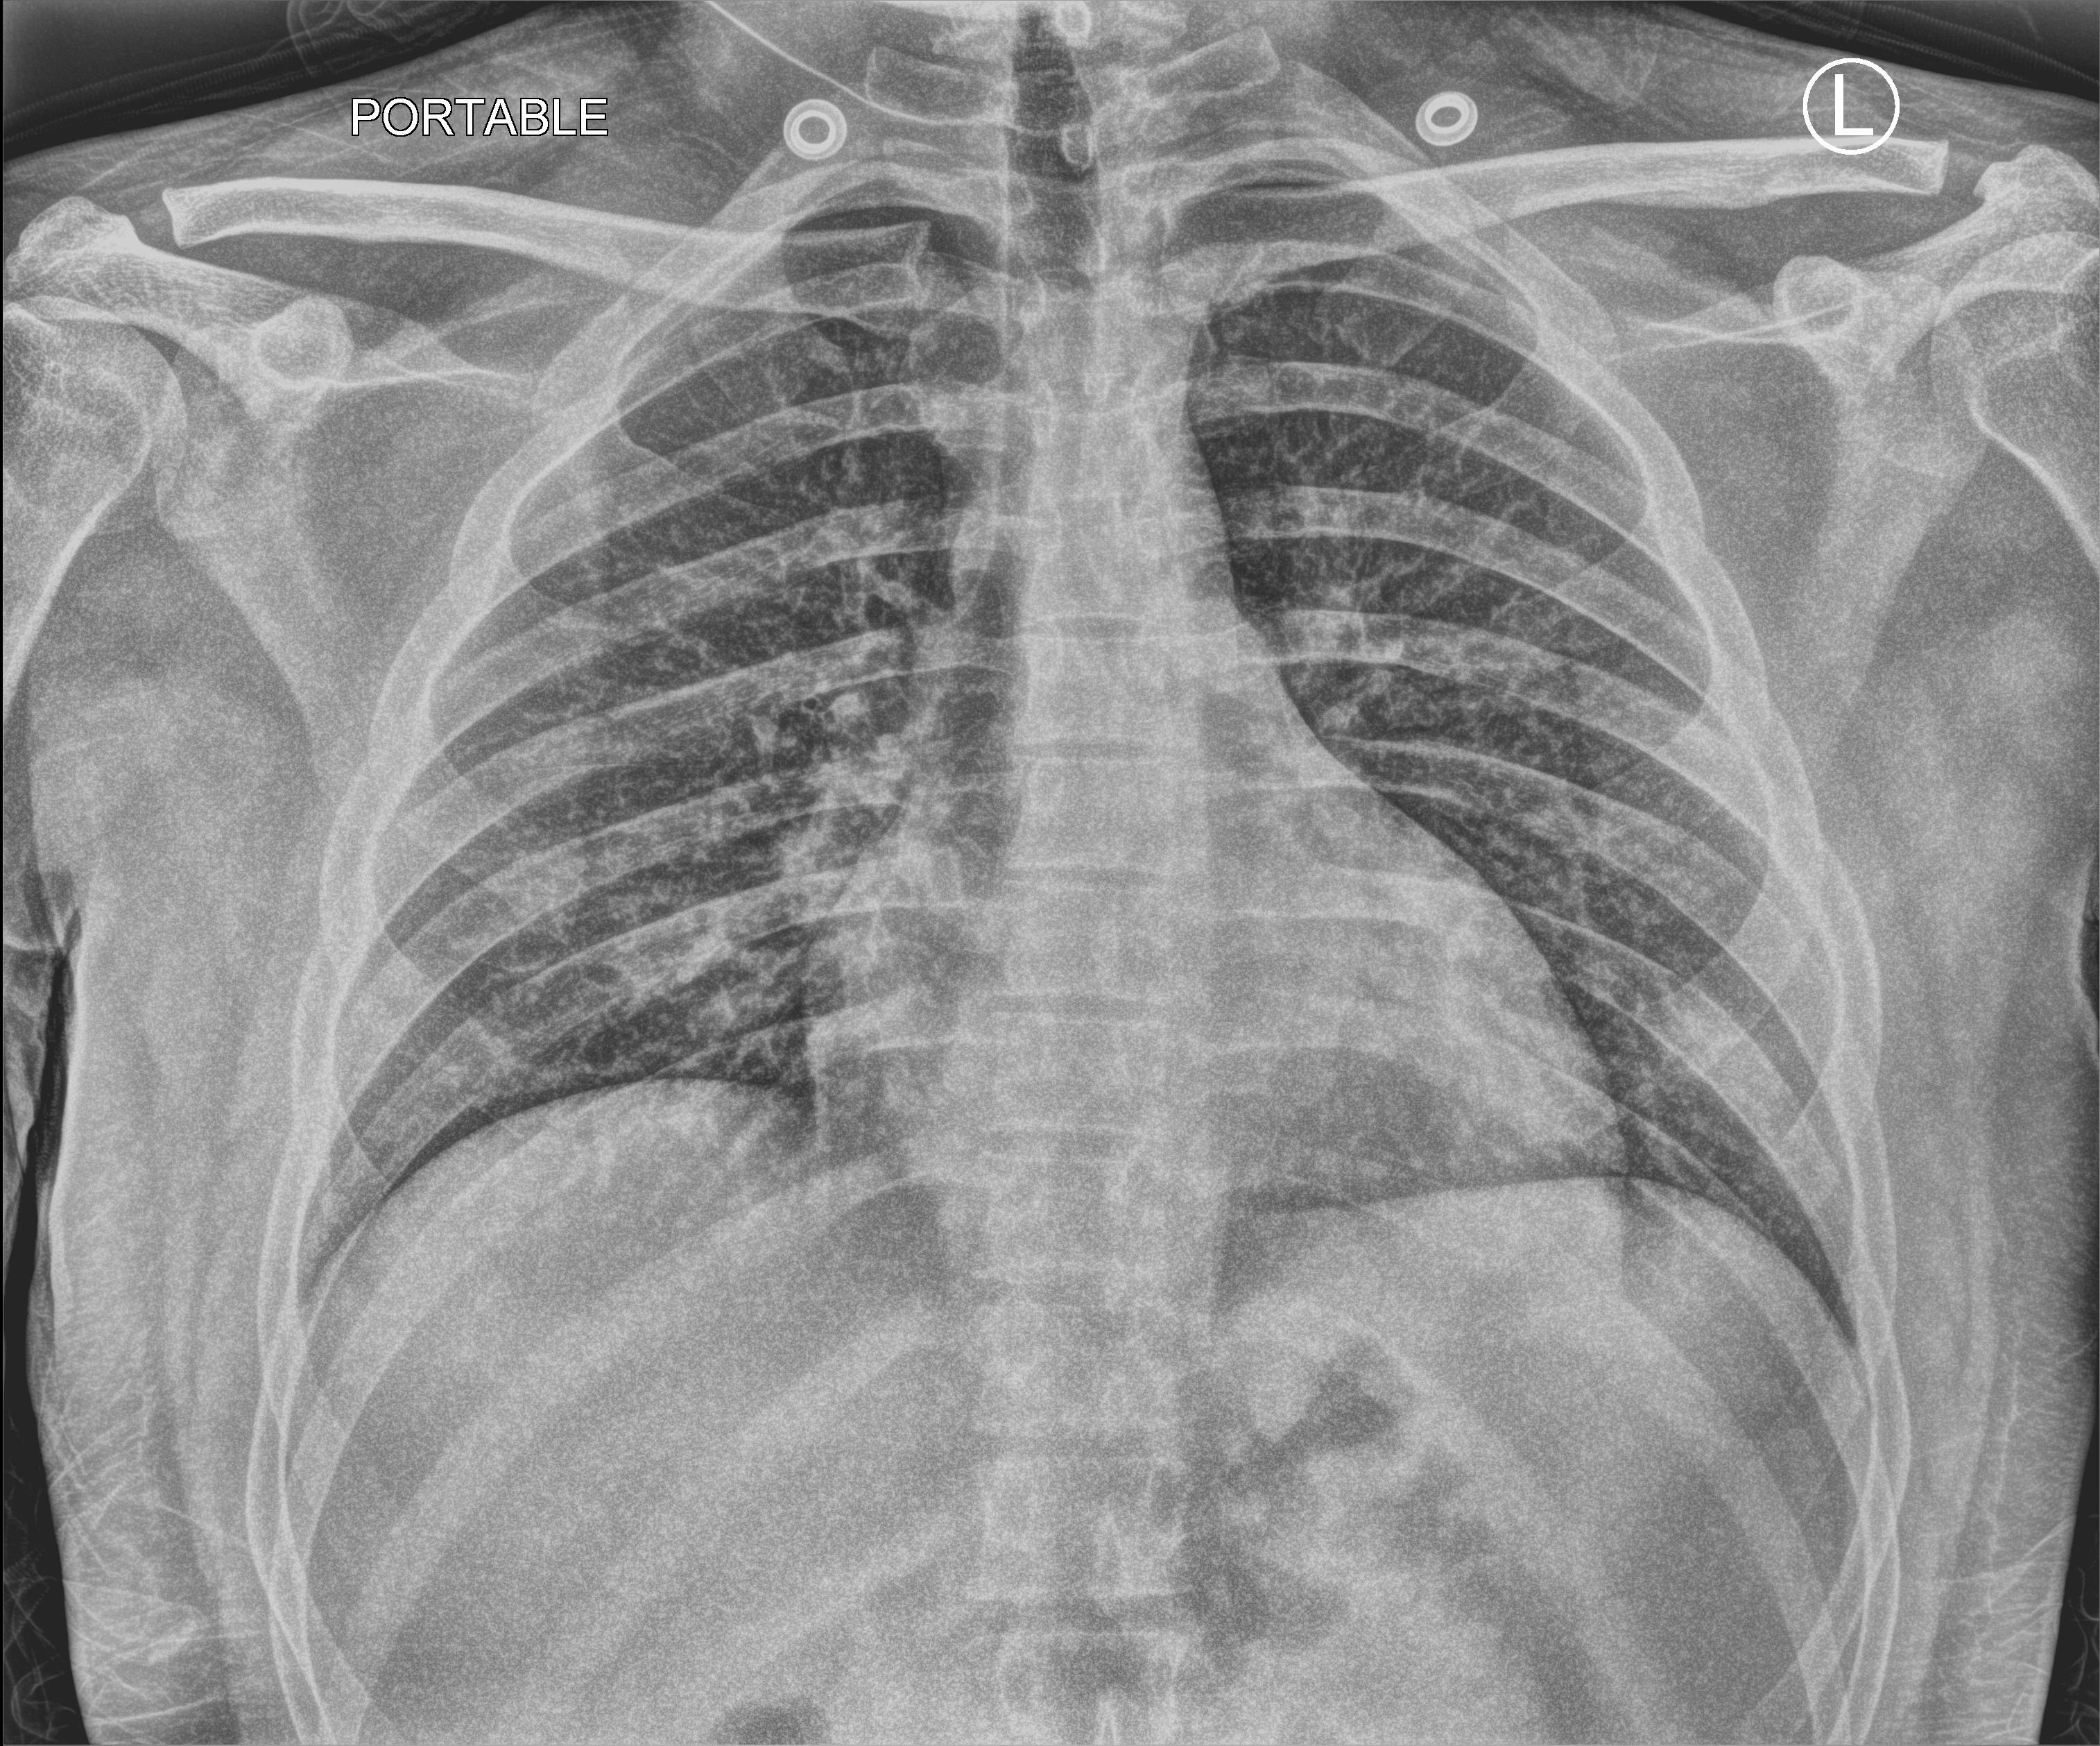
Bedside chest radiograph (computed radiography), anteroposterior (AP) projection. Patient hospitalised with COVID-19; male, aged 18–59 years.
From the hospital-stay record, not from the radiograph (when in the stay this image was taken is not recorded): COPD (admission record): no; admitted to intensive care during this hospital stay: no; mechanically ventilated during this hospital stay: no.